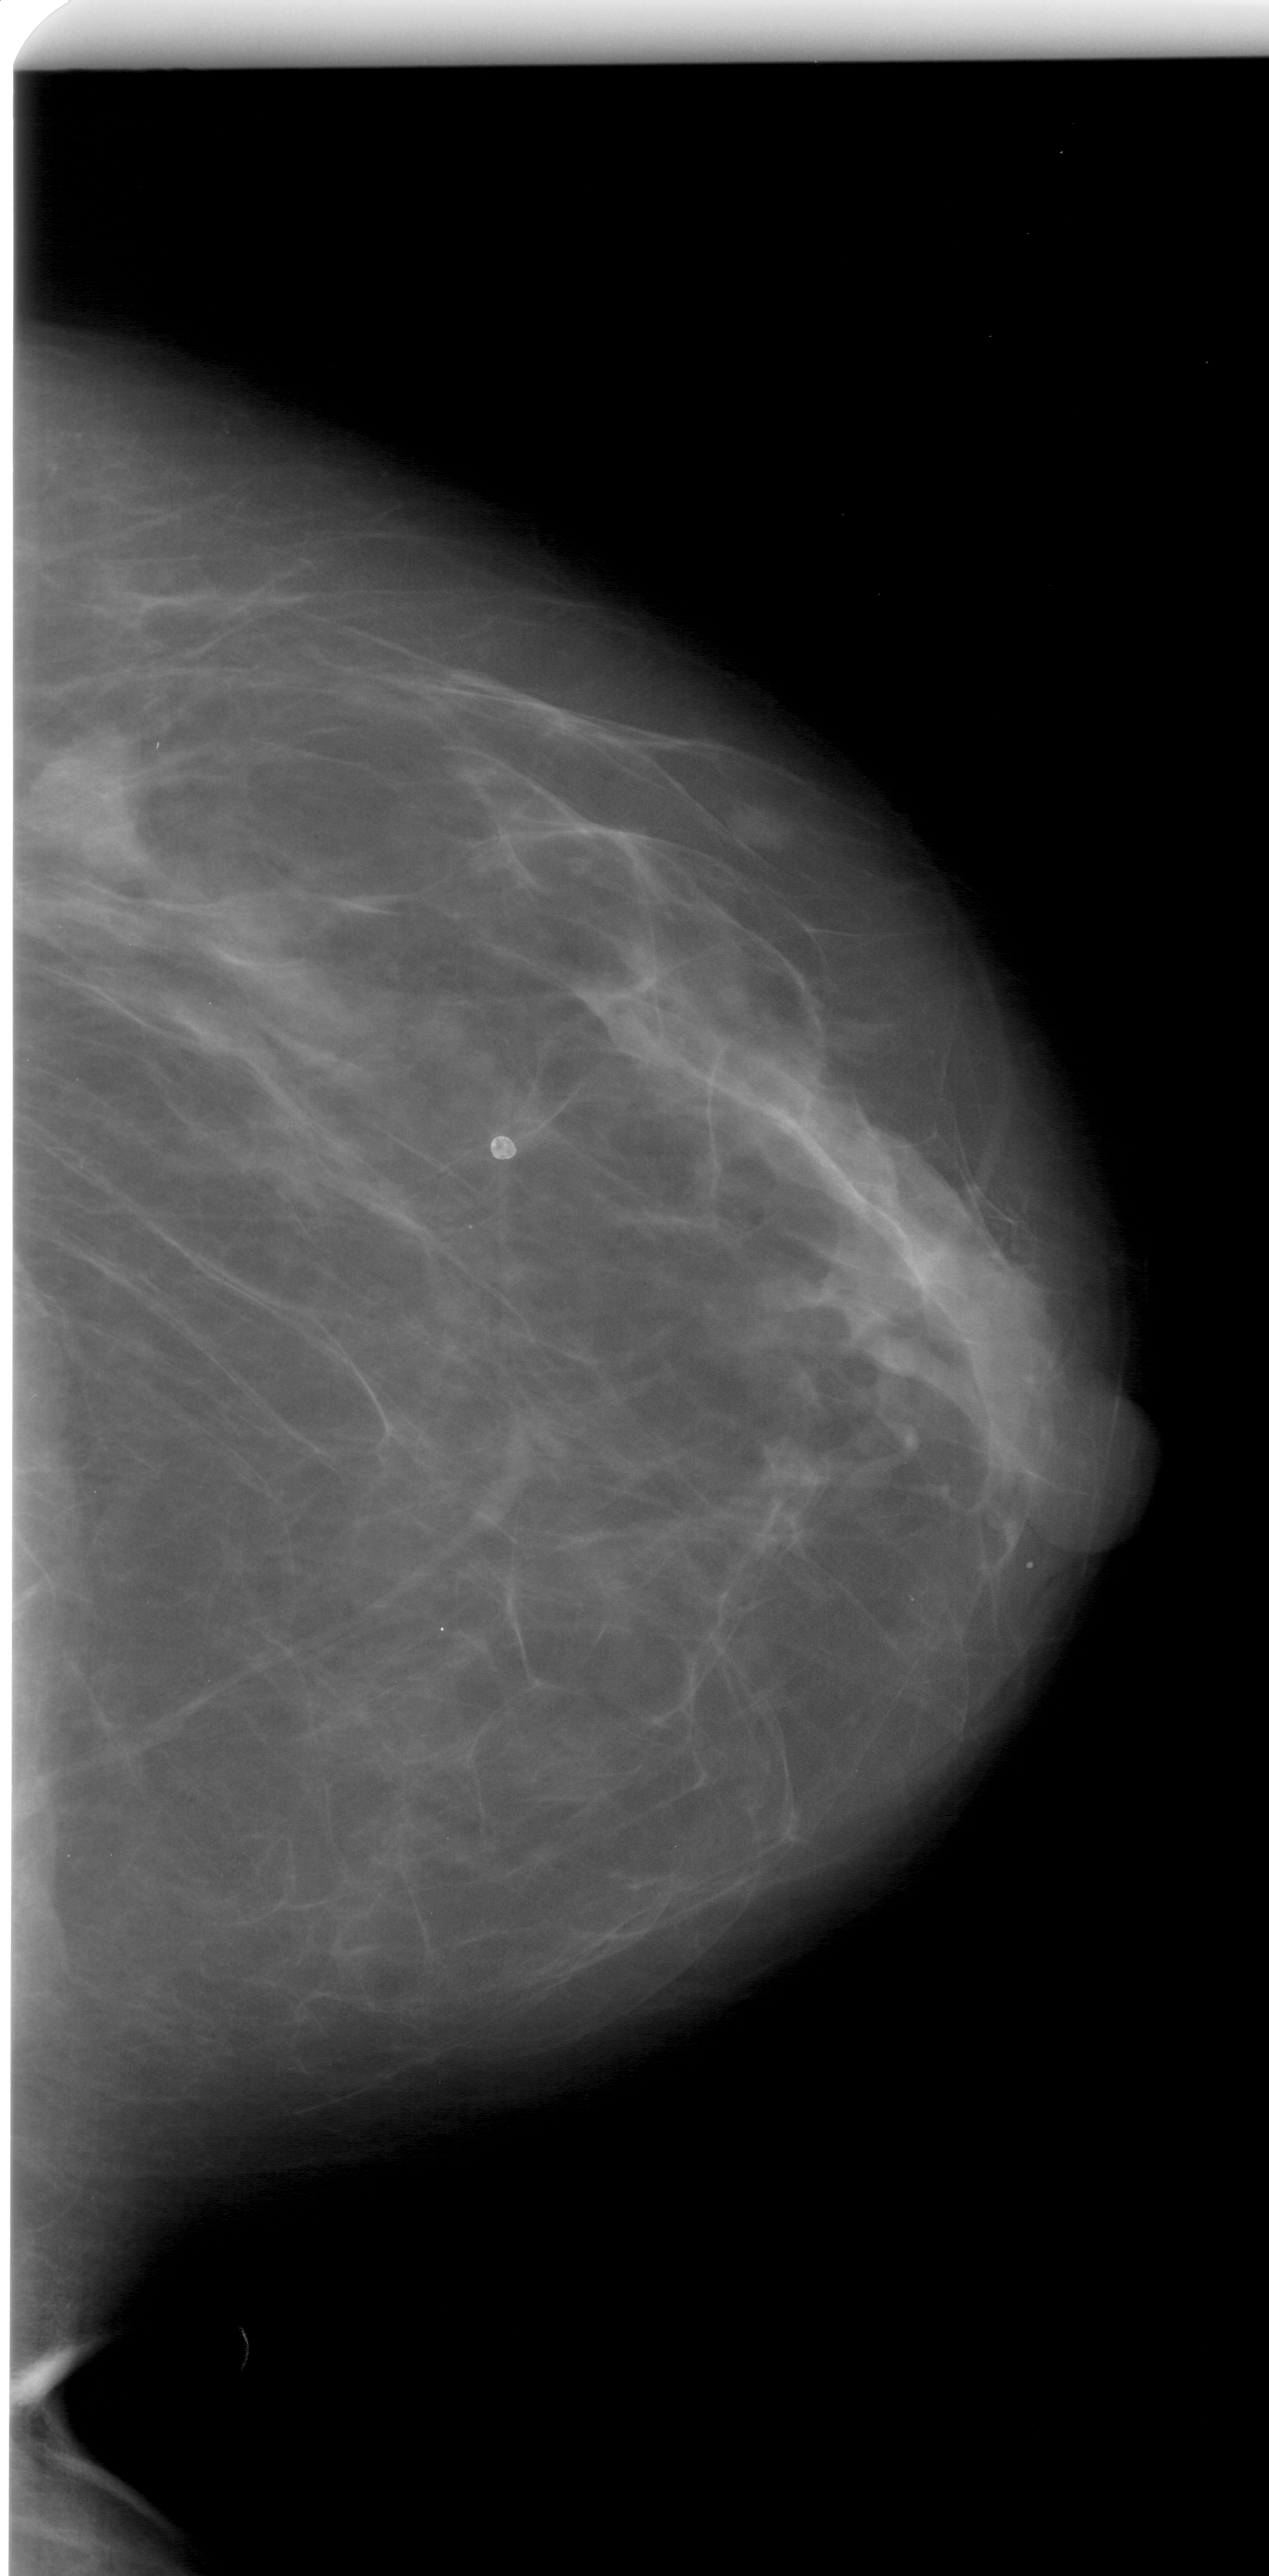
Scanned film-screen mammogram, right breast, CC view, BI-RADS breast density category 1 (scale 1–4).
Radiologist-marked abnormalities on this image: mass, shape lobulated, margins ill defined; BI-RADS assessment category 4; subtlety rating 4 on a 1 (subtle) to 5 (obvious) scale; pathology (as recorded): benign.